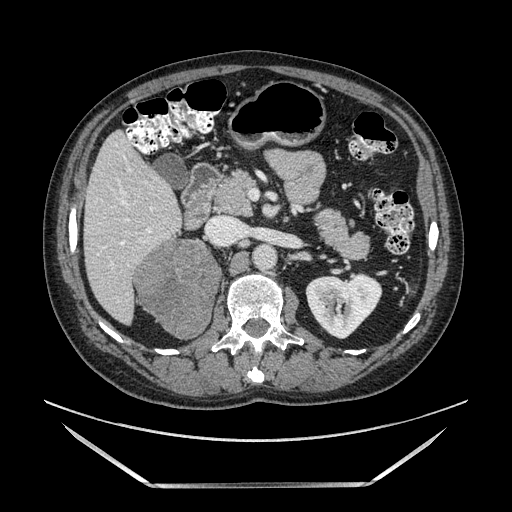
Contrast-enhanced abdominal CT, one axial slice; position 67 of 185 along the scan axis; soft-tissue window (W 400 / L 40 HU); 1.25 mm slice thickness; 512 × 512 image matrix, field of view 440 × 440 mm. Male patient. Case-level facts recorded for this patient, not image findings: diagnosis: adrenocortical carcinoma; tumour side: right adrenal.
Annotated regions visible in this slice (semi-automatically segmented with operator editing):
- mass: bounding box (x1, y1, x2, y2) in pixels: (135, 240, 217, 339)